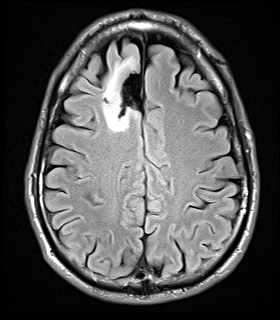
Brain MRI from a brain-tumour surgery series, one axial slice; position 10 of 32 along the scan axis; T2 FLAIR; 5 mm slice thickness; 280 × 320 image matrix. Case-level facts recorded for this patient, not image findings: histopathology: Glial fibroma; tumour location: Right Frontal.
Structures marked on this image (manually delineated by an expert):
- tumour: bounding box <103,57,141,133> (left, top, right, bottom; pixels)